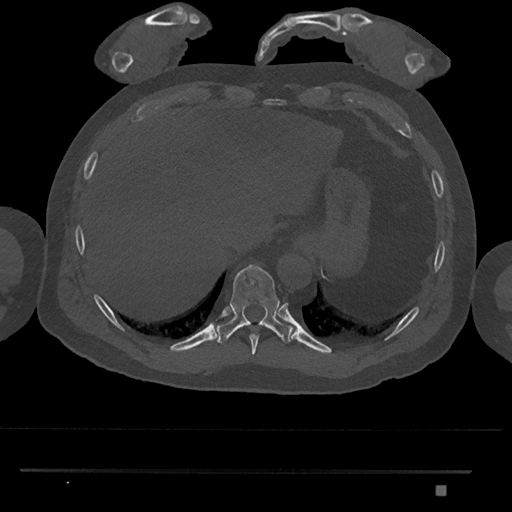
CT including the spine, one axial slice; slice 1016 of 1134 in the series (ordered by position); bone window (W 1800 / L 400 HU); 0.5 mm slice thickness; 512 × 512 image matrix, field of view 429 × 429 mm. Patient: male, 65 years. Case-level facts recorded for this patient, not image findings: primary cancer: prostate.
Structures marked on this image (semi-automatically segmented with operator editing):
- T10 vertebra: bounding box (x1, y1, x2, y2) in pixels: (215, 264, 291, 344)
- T9 vertebra: (250, 334, 259, 360)